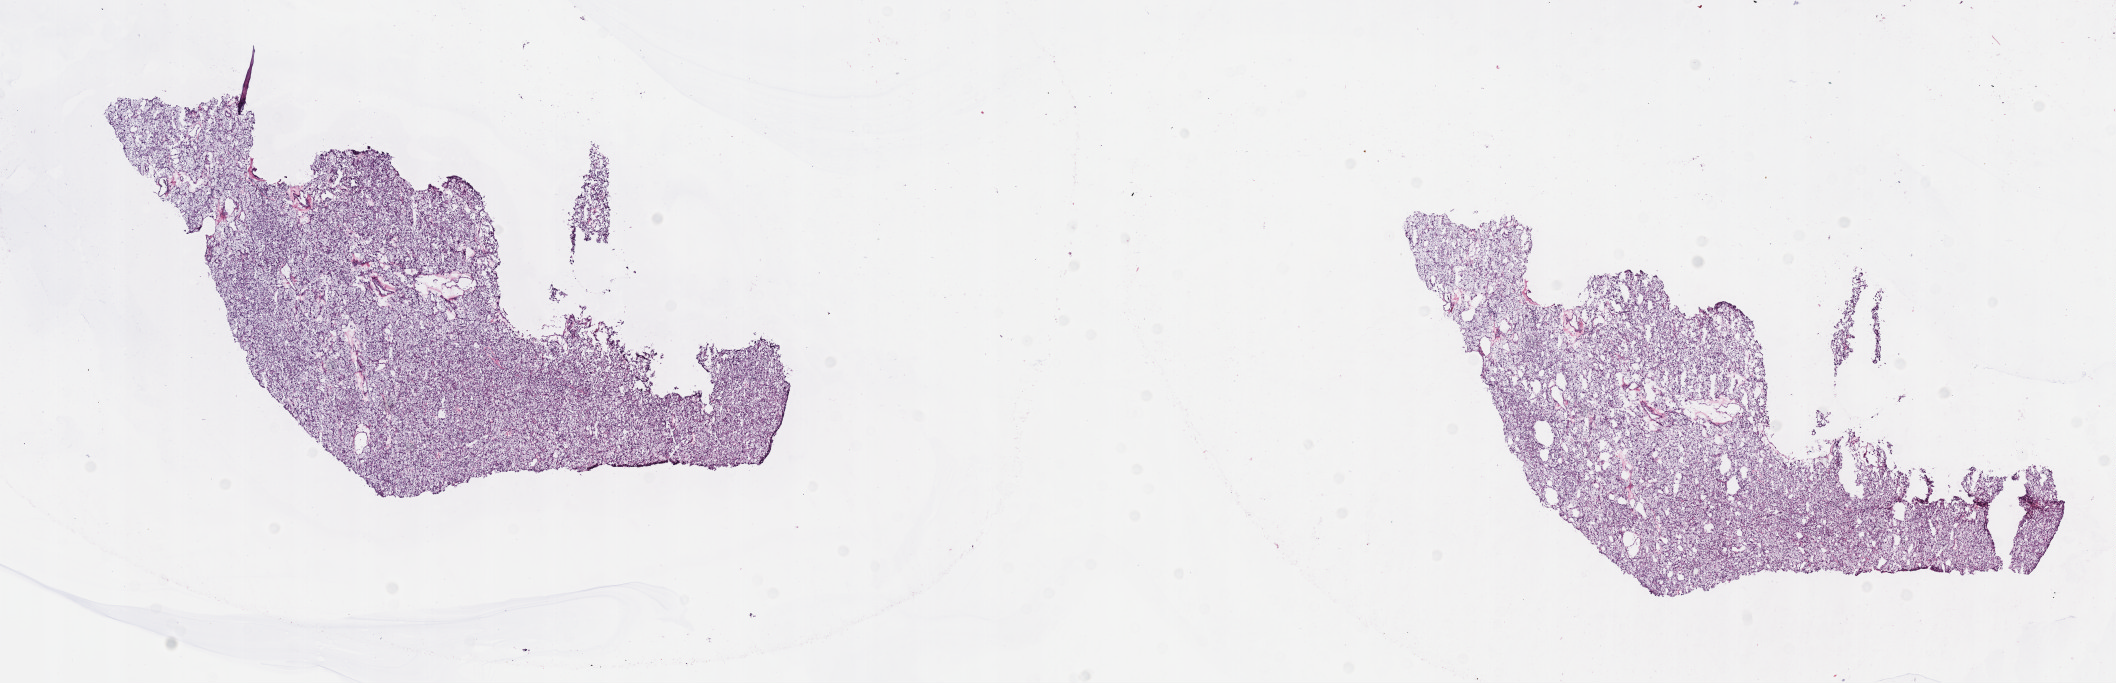
Whole-slide histology image, H&E-stained — a low-resolution overview of the entire scanned area, about 17.1 x 5.5 mm. Frozen section from the top of the tissue portion. Sample: primary tumour, kidney. Male patient; age at initial diagnosis 37 years. Histologic grade: G2 (moderately differentiated). Composition of this section per pathologist review: tumour cells 90%, tumour nuclei 95%, normal cells 0%, stromal cells 10%, necrosis 0%. Inflammatory infiltration, as recorded: lymphocyte infiltration 2%, monocyte infiltration 1%, neutrophil infiltration 0%.
Histologic diagnosis: Clear cell adenocarcinoma, NOS. AJCC pathologic stage: III (7th edition). Laterality: left.